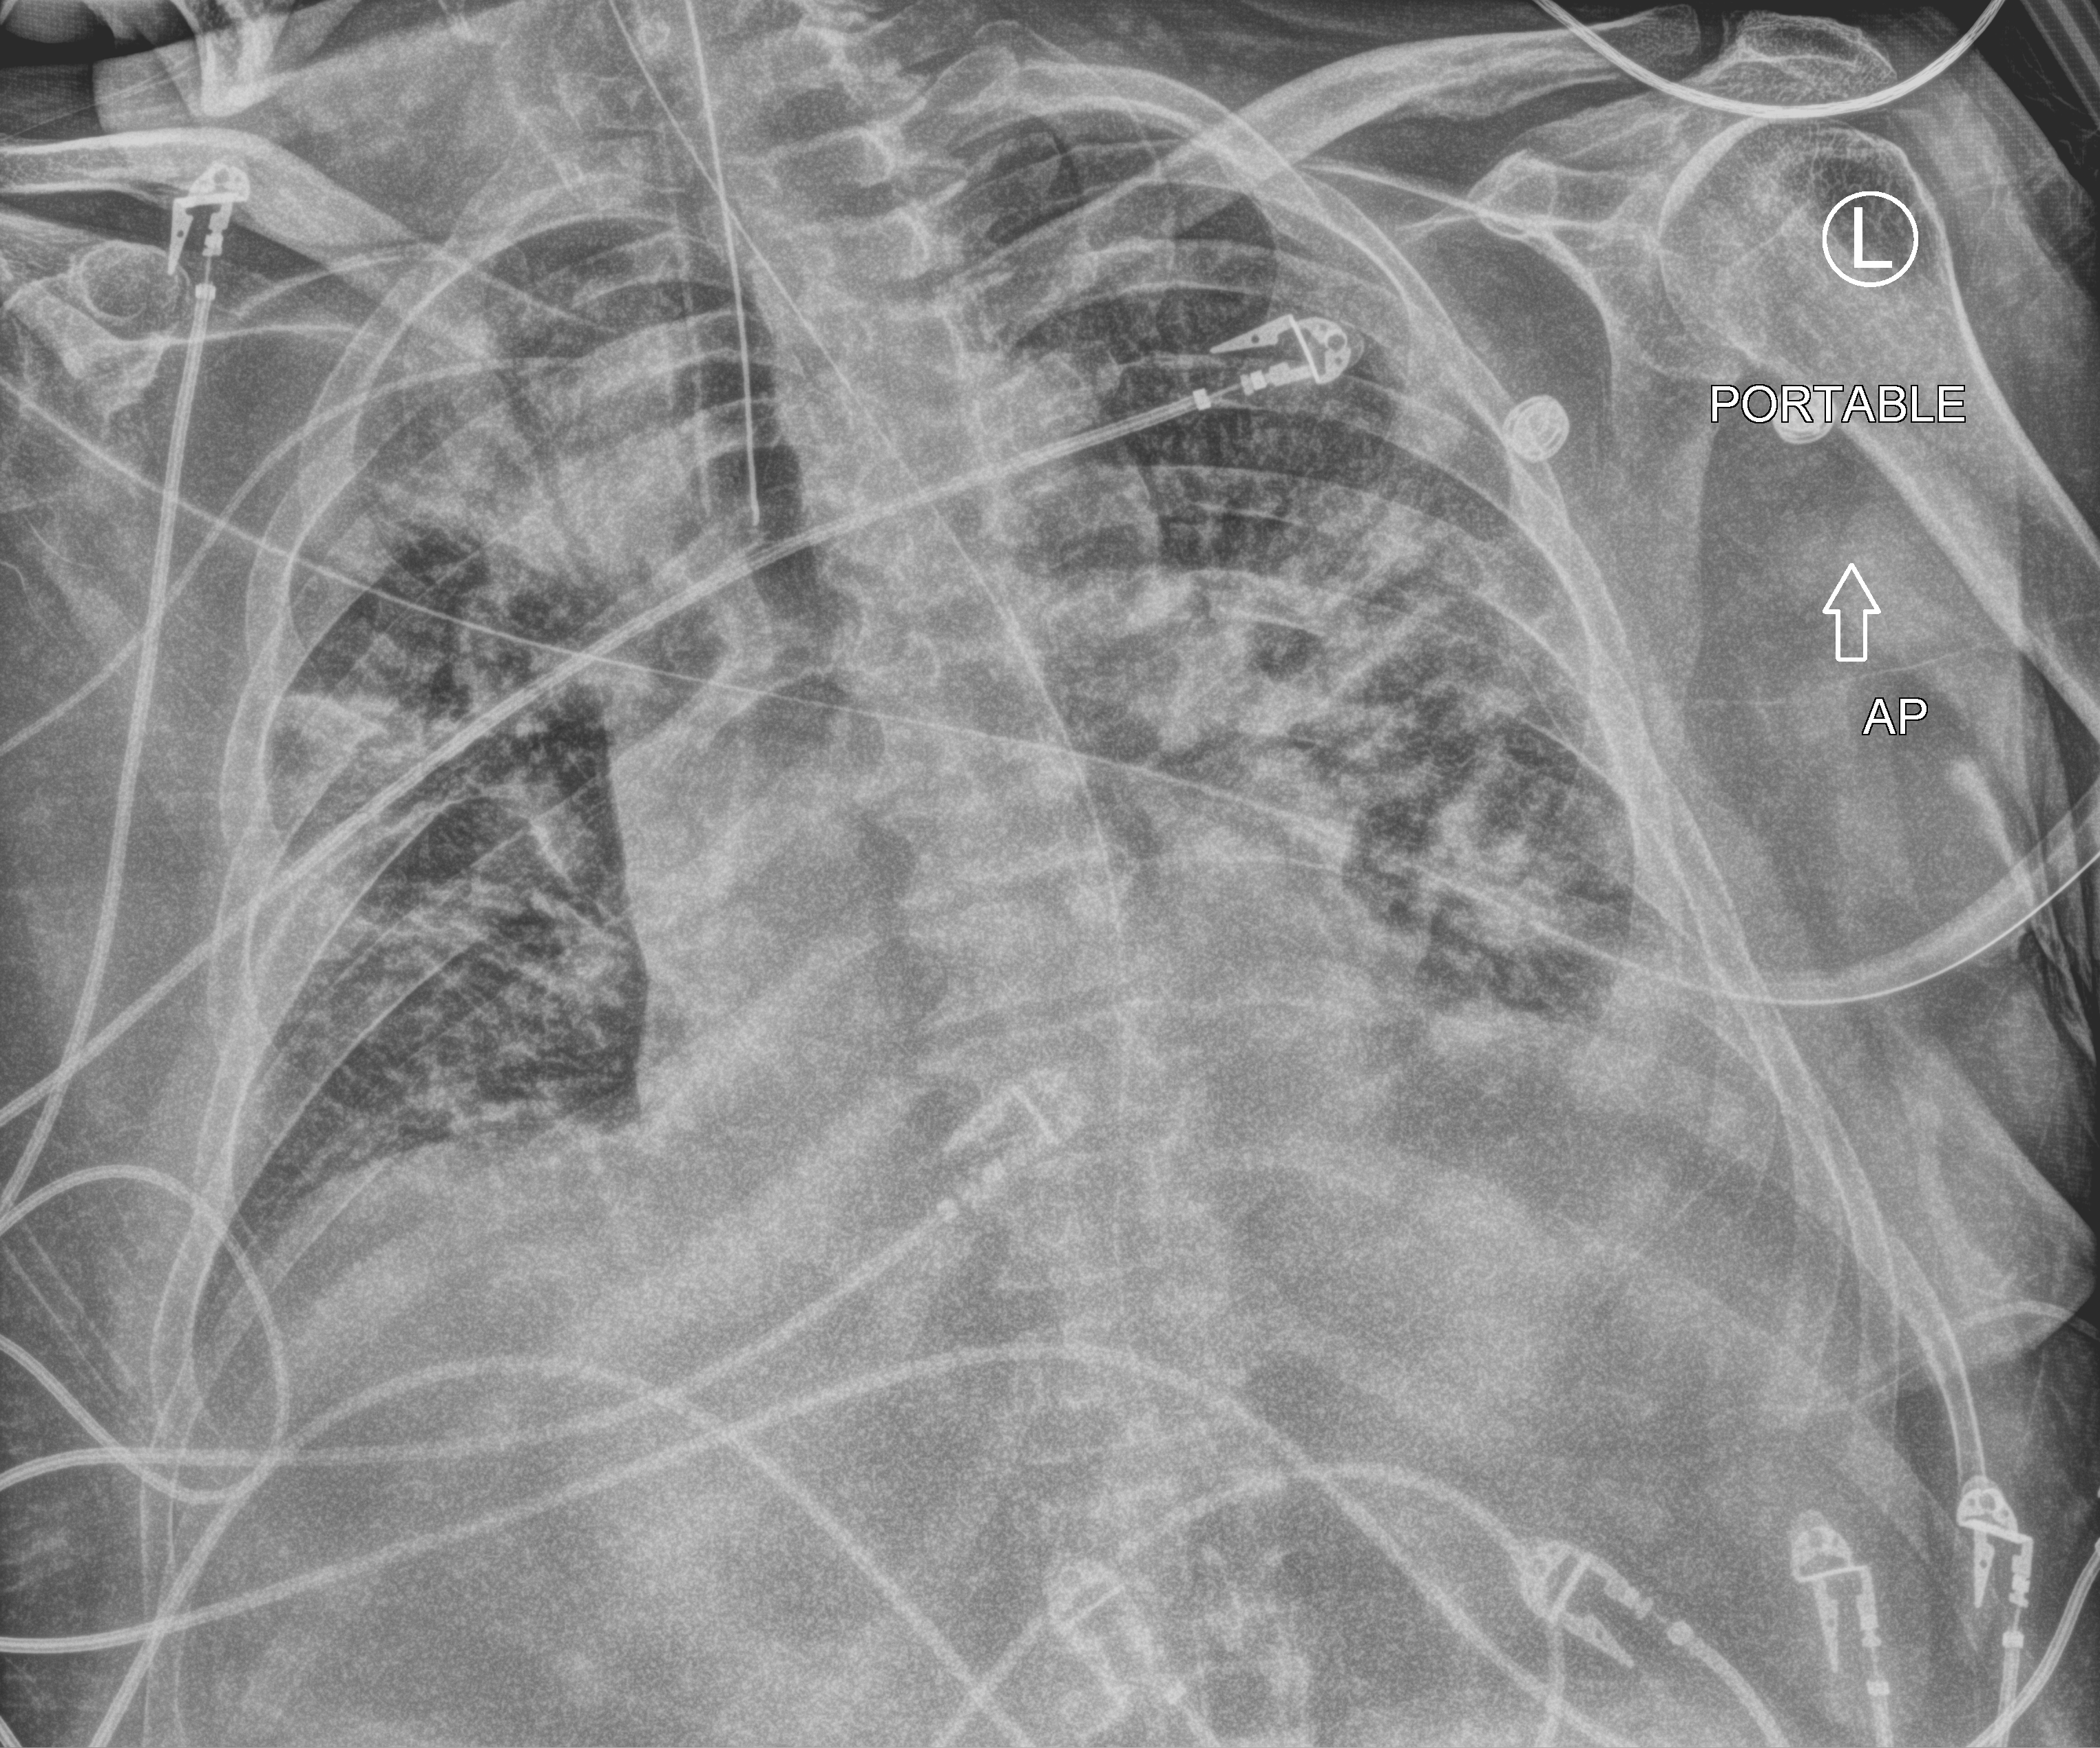
Chest X-ray (portable). Male patient hospitalised with COVID-19, age 60–74 years.
From the hospital-stay record, not from the radiograph (when in the stay this image was taken is not recorded): mechanically ventilated during this hospital stay: yes.